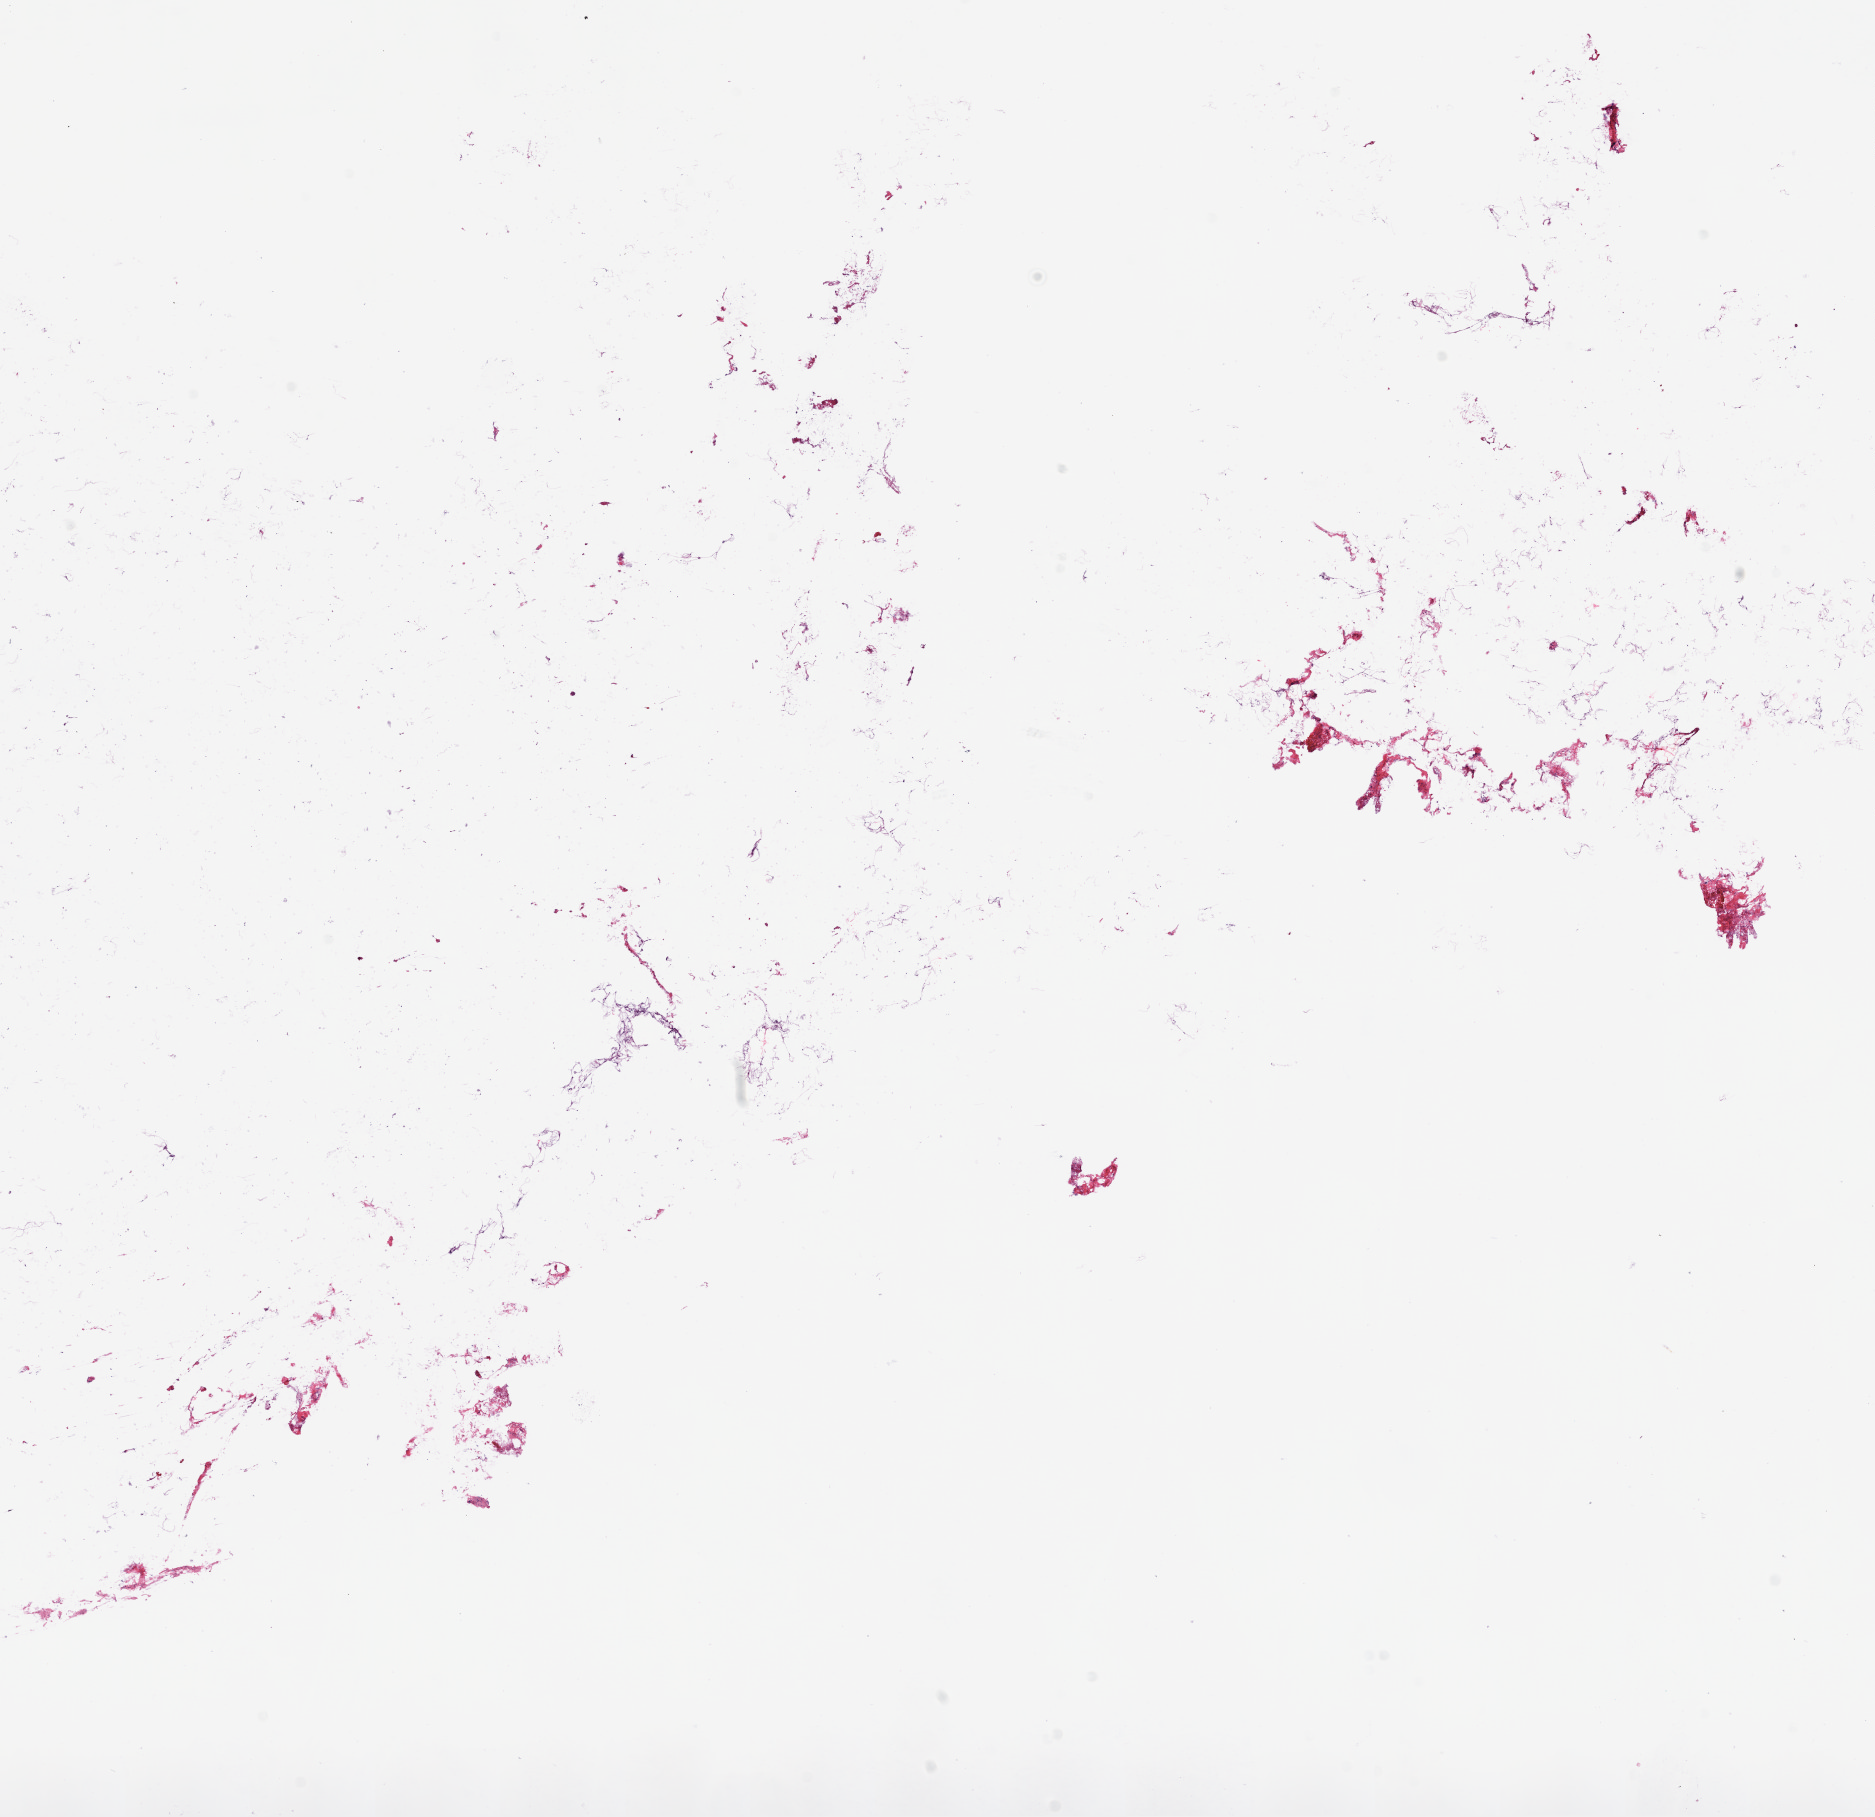
Digitized H&E tissue section (whole slide) — whole scanned area (about 15.0 x 14.6 mm, acquisition: 20x scan) shown as a low-resolution overview, frozen section from the bottom of the tissue portion, solid tissue normal (non-tumour tissue) sample from the kidney. Female, age 59 years at initial diagnosis.
This section: solid tissue normal (non-tumour) sample from the same patient. Patient diagnosis: Papillary adenocarcinoma, NOS.